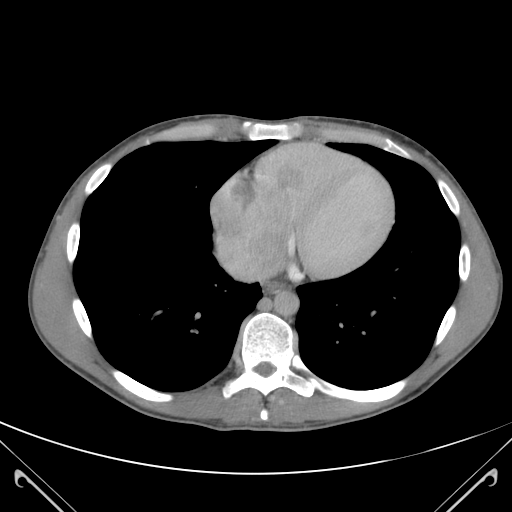
Contrast-enhanced abdominal CT (liver protocol), one axial slice; position 114 of 118 along the scan axis; soft-tissue window (W 400 / L 40 HU); 512 × 512 image matrix. Case-level facts recorded for this patient, not image findings: diagnosis: hepatocellular carcinoma (patient treated with transarterial chemoembolisation; whether this scan precedes or follows treatment is not stated here); TNM stage (as recorded): Stage-IIIB; Child-Pugh class: A; tumour nodularity: uninodular.
Structures marked on this image (semi-automatically segmented with operator editing):
- abdominal aorta: bounding box <275,291,298,314> (left, top, right, bottom; pixels)